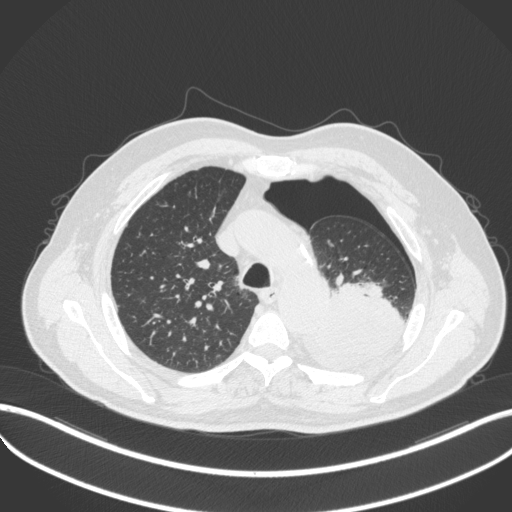
Chest CT, one axial slice; slice 376 of 466 in the series (ordered by position); reconstruction kernel B31f; 120 kVp; lung window (W 1500 / L -600 HU); 1 mm slice thickness; 512 × 512 image matrix, field of view 400 × 400 mm. Patient: male, 76 years. From the clinical record (not read from this slice): clinical TNM (as recorded): T3 N0 M1b.
Structures marked on this image (rectangle marked by the reading radiologist):
- lung tumour (recorded histology: adenocarcinoma): bounding box <301,275,407,375> (left, top, right, bottom; pixels)